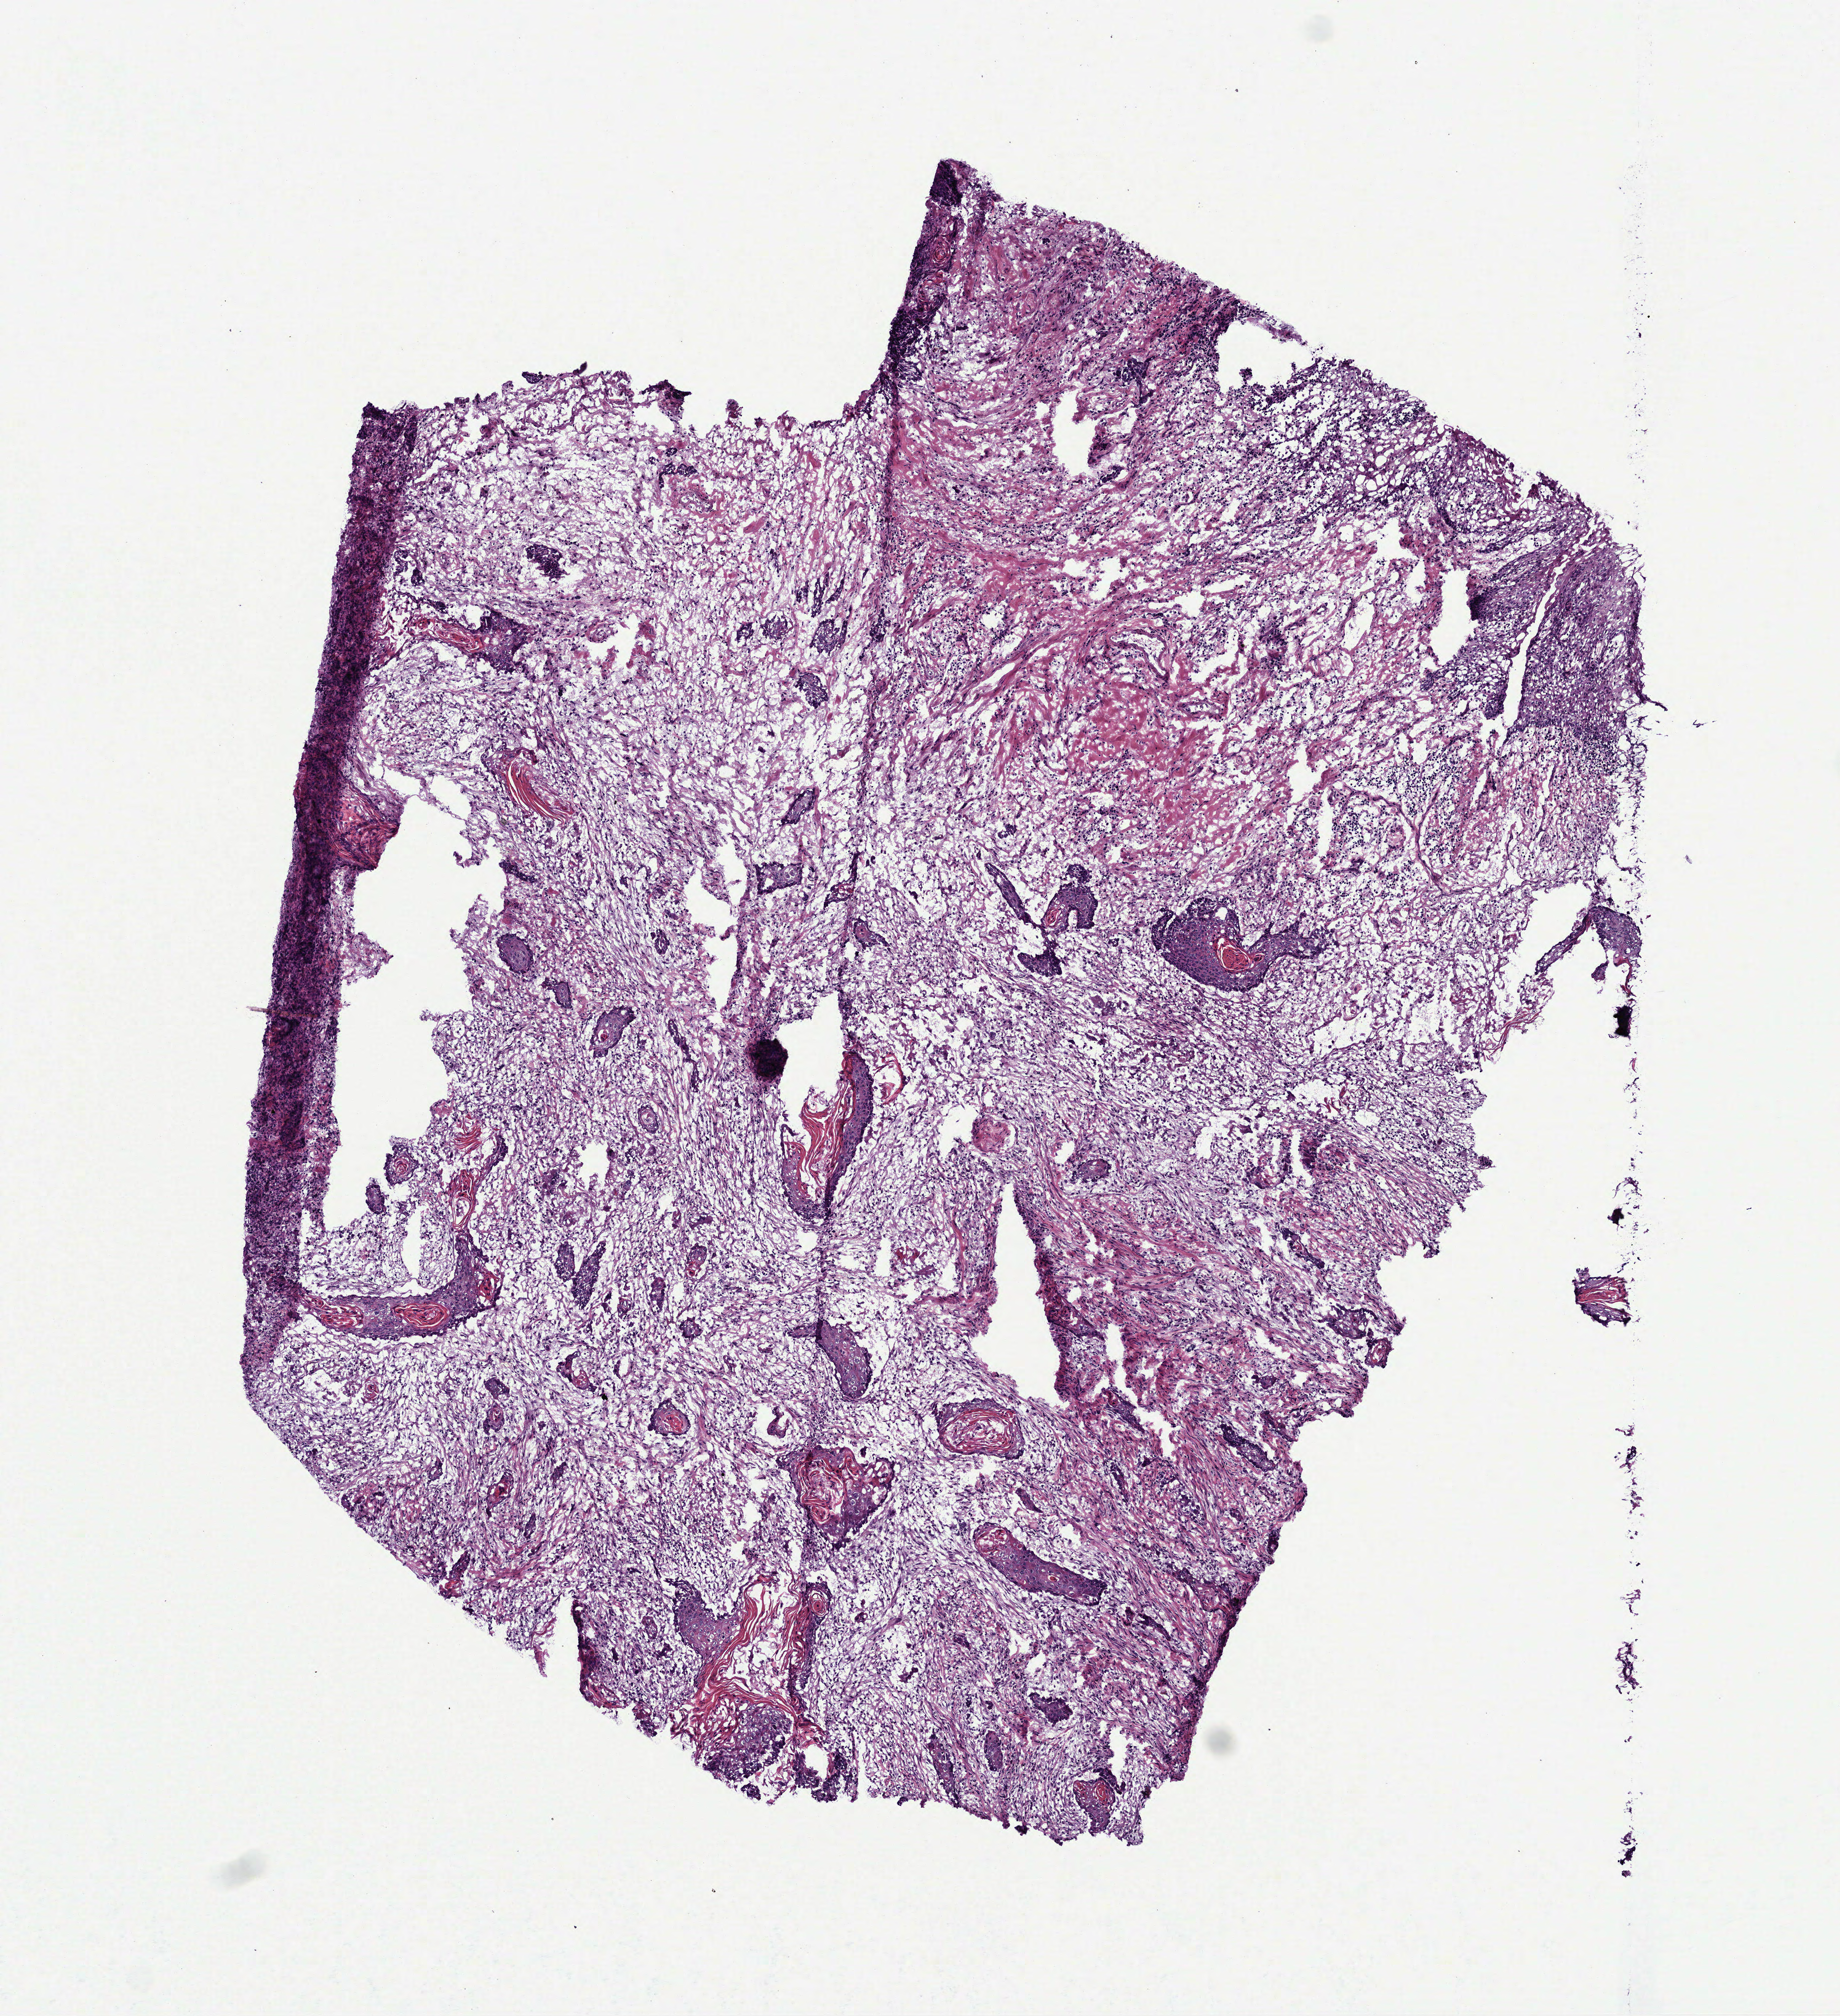
Whole-slide histology image, H&E — low-resolution overview of the scanned area, about 5.6 x 6.1 mm (acquisition: 40x scan); frozen section from the top of the tissue portion; primary tumour sample from the head and neck. Male patient; age at initial diagnosis 61 years. Histologic grade: G2 (moderately differentiated). Composition of this section per pathologist review: tumour cells 25%, tumour nuclei 60%, normal cells 0%, stromal cells 75%, necrosis 0%.
• diagnosis: Squamous cell carcinoma, NOS (tongue, NOS)
• lymph nodes positive (case pathology): 0 of 45 examined
• AJCC pathologic stage: IVA (7th edition)
• TNM: T4a N0